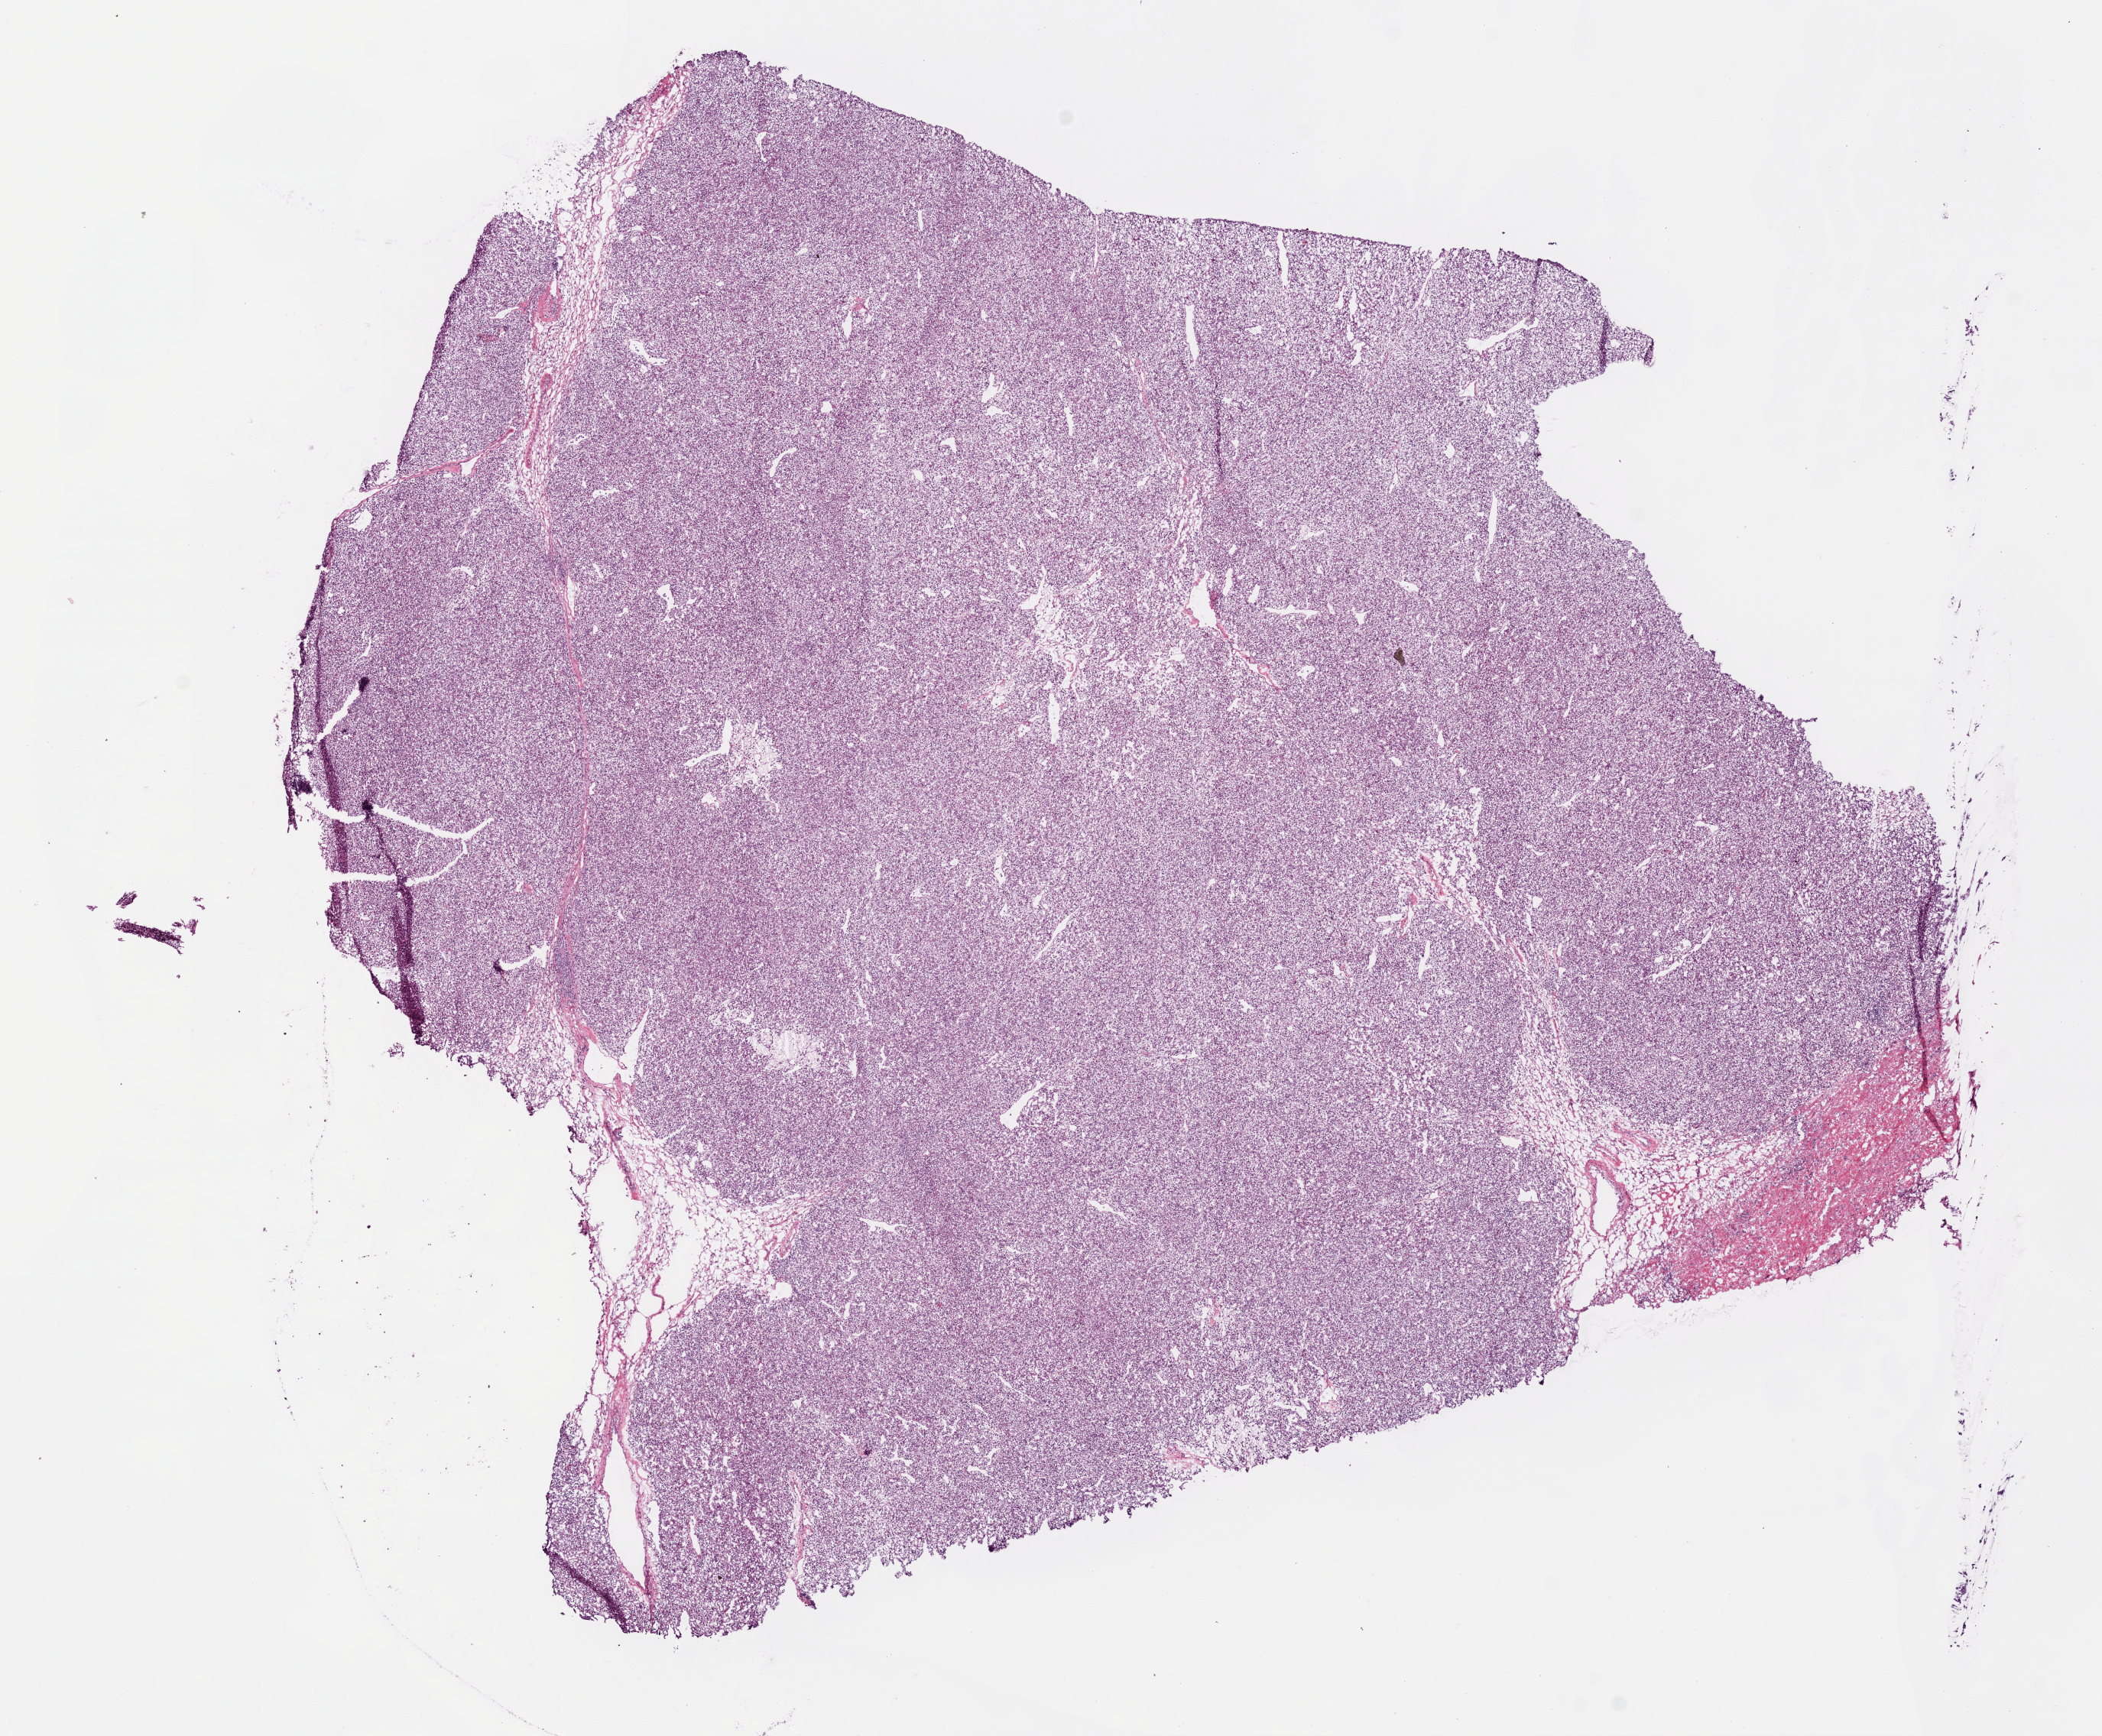
Hematoxylin and eosin (H&E) stained whole-slide image — whole scanned area (about 11.0 x 9.1 mm) shown as a low-resolution overview. Frozen section. Kidney, primary tumour sample. Patient: female, age at initial diagnosis 63 years. Histologic grade: G3 (poorly differentiated). Composition of this section per pathologist review: tumour cells 90%, tumour nuclei 90%, normal cells 0%, stromal cells 10%, necrosis 0%.
* diagnosis: Clear cell adenocarcinoma, NOS
* AJCC pathologic stage: I (6th edition)
* TNM: T1a N0 M0